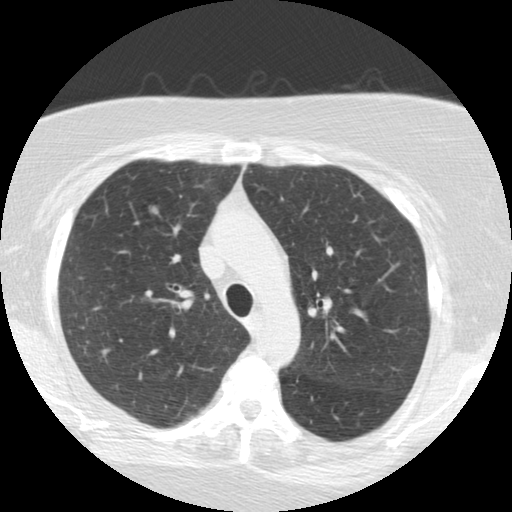
Axial slice from a low-dose chest CT screening exam. Second screening round (one year after baseline). Lung window (W 1500 / L -600 HU). 2.5 mm slice thickness. Standard (soft-tissue) reconstruction kernel (STANDARD). 512 × 512 image matrix. Female, age 64 years at enrolment.
Expert-annotated lung lesion, box from (x=132, y=195) to (x=170, y=233) px. Screening reader's record for this exam (one nodule recorded; not confirmed to be the boxed lesion): non-calcified nodule or mass ≥4 mm, right upper lobe, 8 × 7 mm, smooth margins, soft tissue attenuation, pre-existing on the prior screen: no.